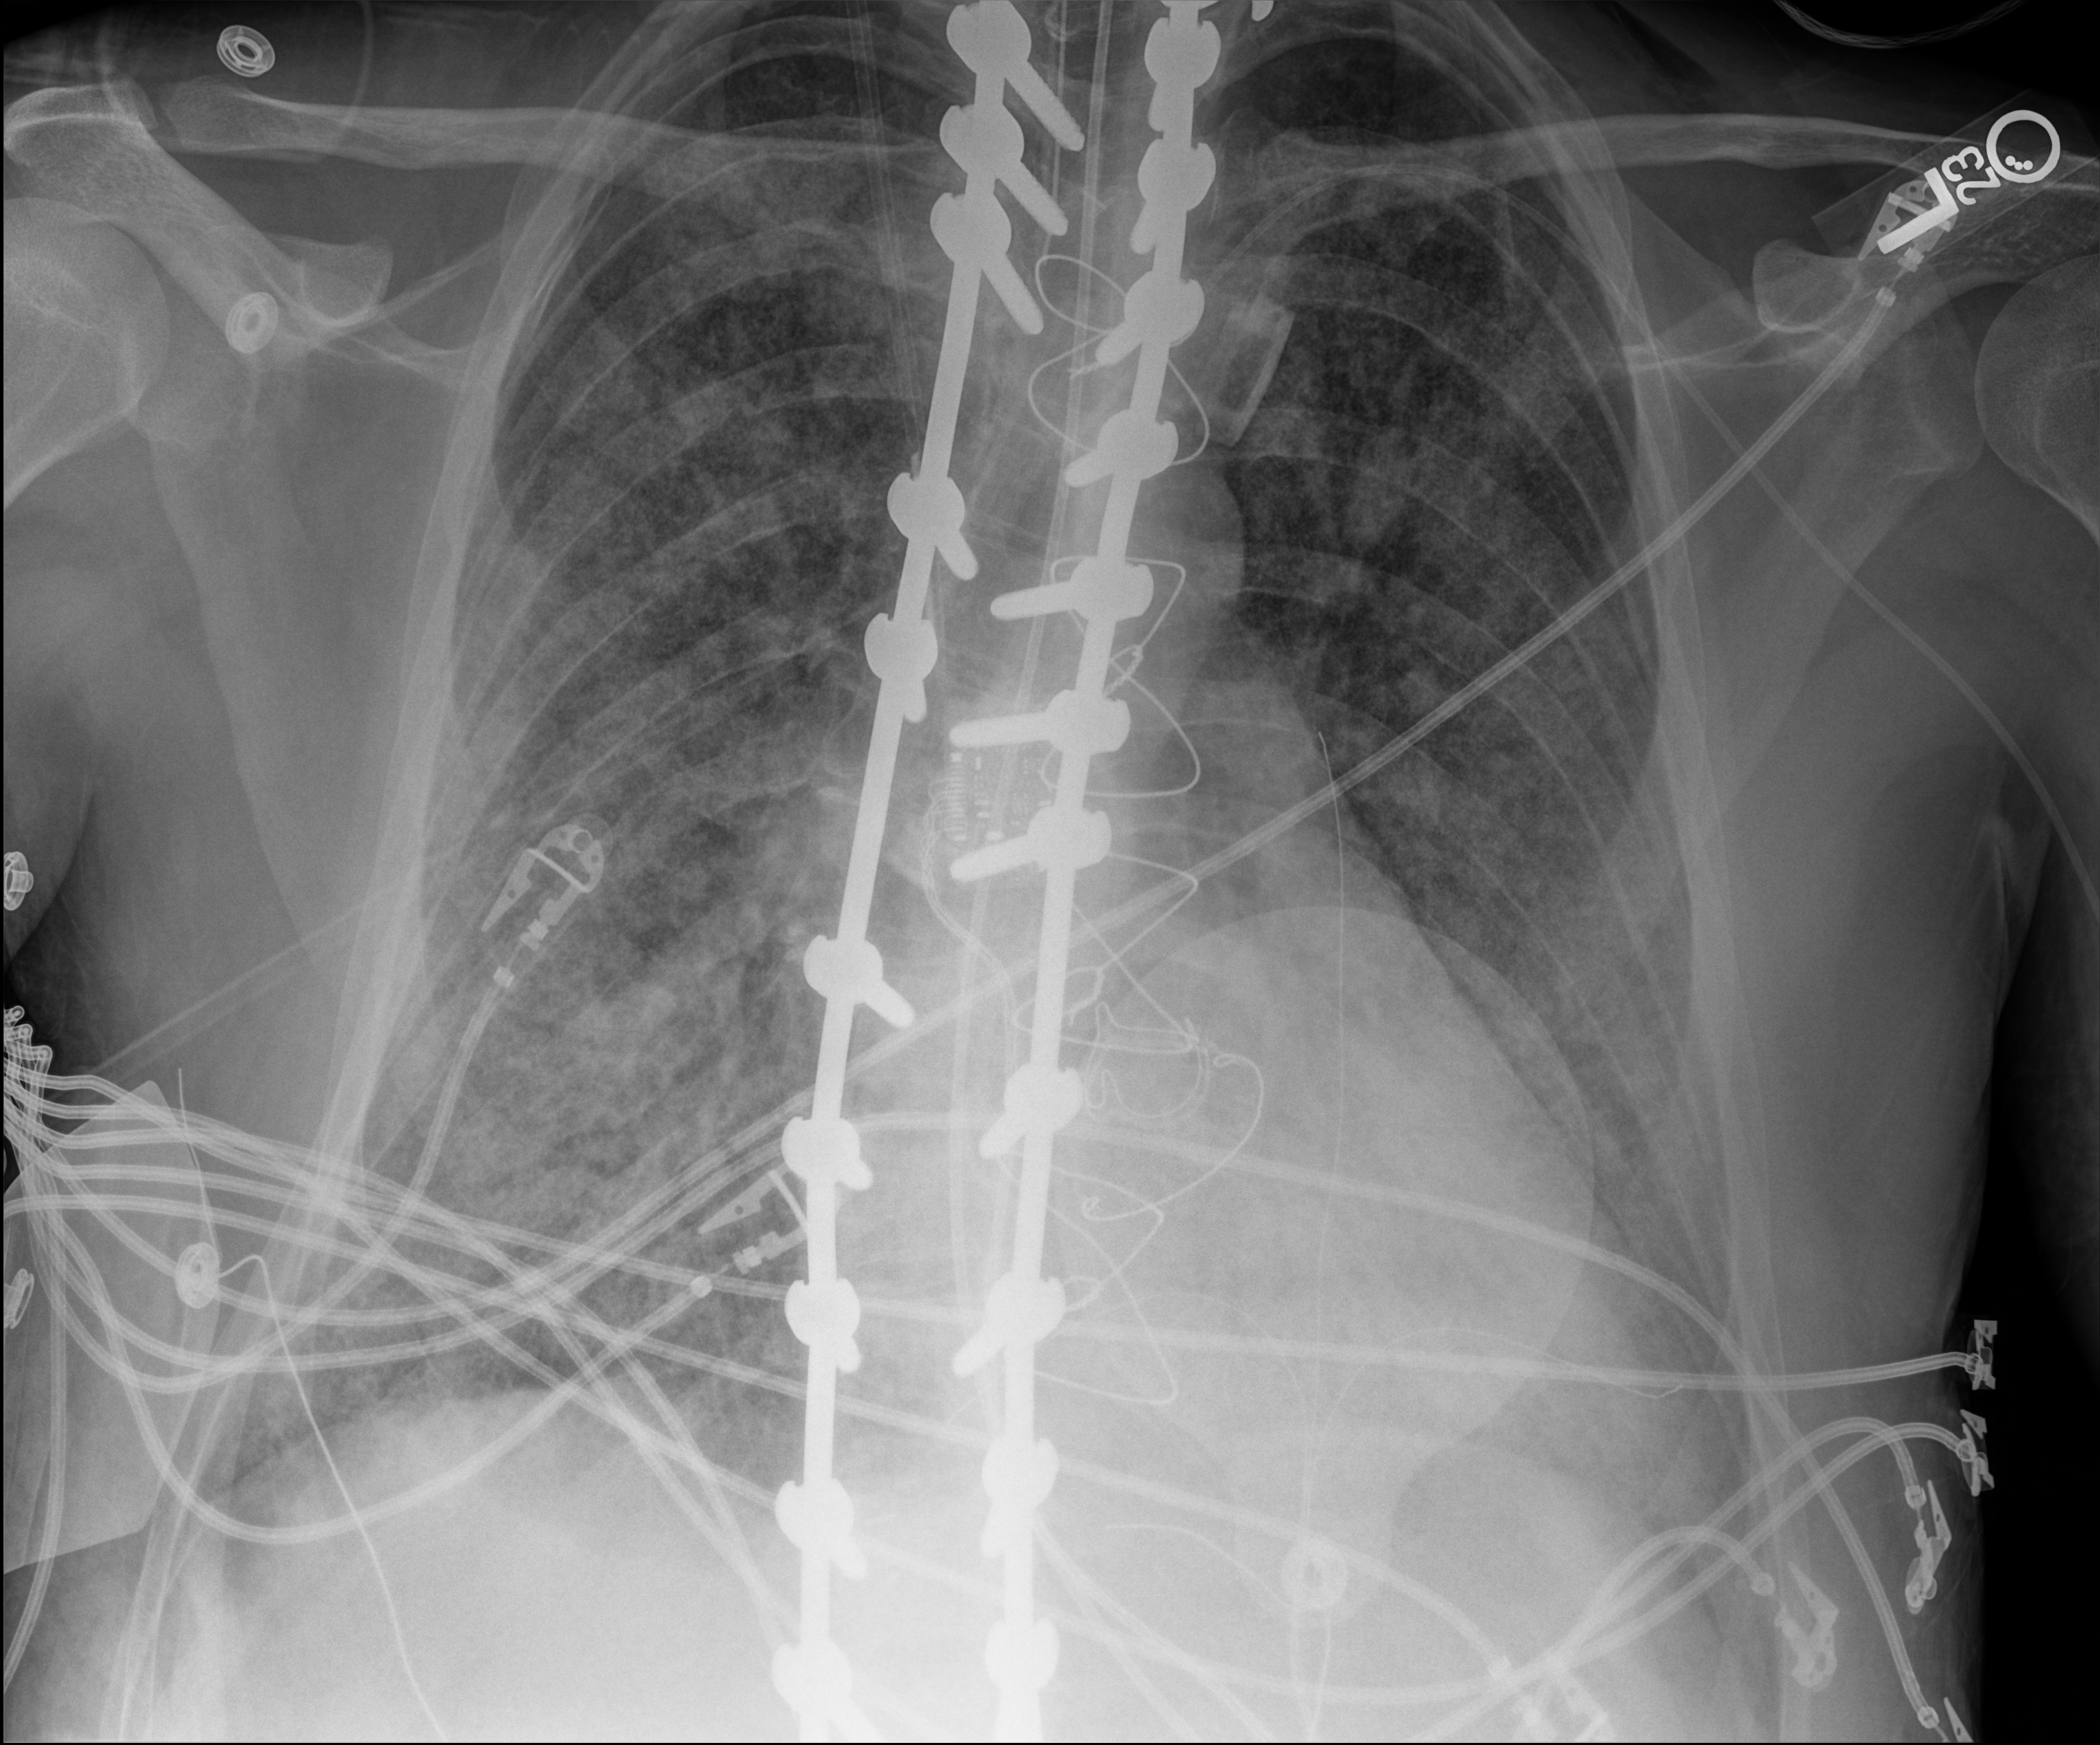
Portable chest radiograph, anteroposterior (AP) projection. Adult patient hospitalised with COVID-19, age 18–59 years.
From the hospital-stay record, not from the radiograph (when in the stay this image was taken is not recorded):
- admitted to intensive care during this hospital stay: yes